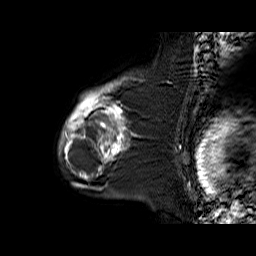
Breast MRI (dynamic contrast-enhanced), one sagittal slice; position 48 of 60 along the scan axis; dynamic contrast-enhanced series, time point 2 of 6 at this slice position (early post-contrast); 1.5 T; TE 6.3 ms, TR 32.9 ms; 256 × 256 image matrix, field of view 200 × 200 mm. Female patient. Case-level facts recorded for this patient, not image findings: setting: breast cancer imaged before/during neoadjuvant chemotherapy; receptor status: triple-negative.
Outlined on this slice (semi-automatically segmented with operator editing):
- analysis volume of interest (the breast-tissue region the enhancement analysis was run in; not a lesion): box from (x=59, y=77) to (x=145, y=170) px
- tumour enhancement mask (voxels above the 100 % enhancement threshold inside the analysis volume of interest): (x=59, y=78)–(x=125, y=170)